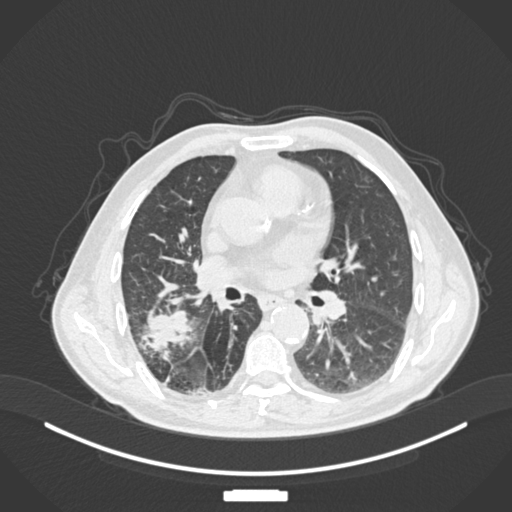
Chest CT, one axial slice. Slice 85 of 201 in the series (ordered by position). Reconstruction kernel B30f. 120 kVp. Lung window (W 1500 / L -600 HU). 1 mm slice thickness. 512 × 512 image matrix, field of view 400 × 400 mm. Male patient, age 72 years. From the clinical record (not read from this slice): clinical TNM (as recorded): T3 N2 M0.
Structures marked on this image (rectangle marked by the reading radiologist):
- lung tumour (recorded histology: adenocarcinoma): bounding box <135,301,194,353> (left, top, right, bottom; pixels)